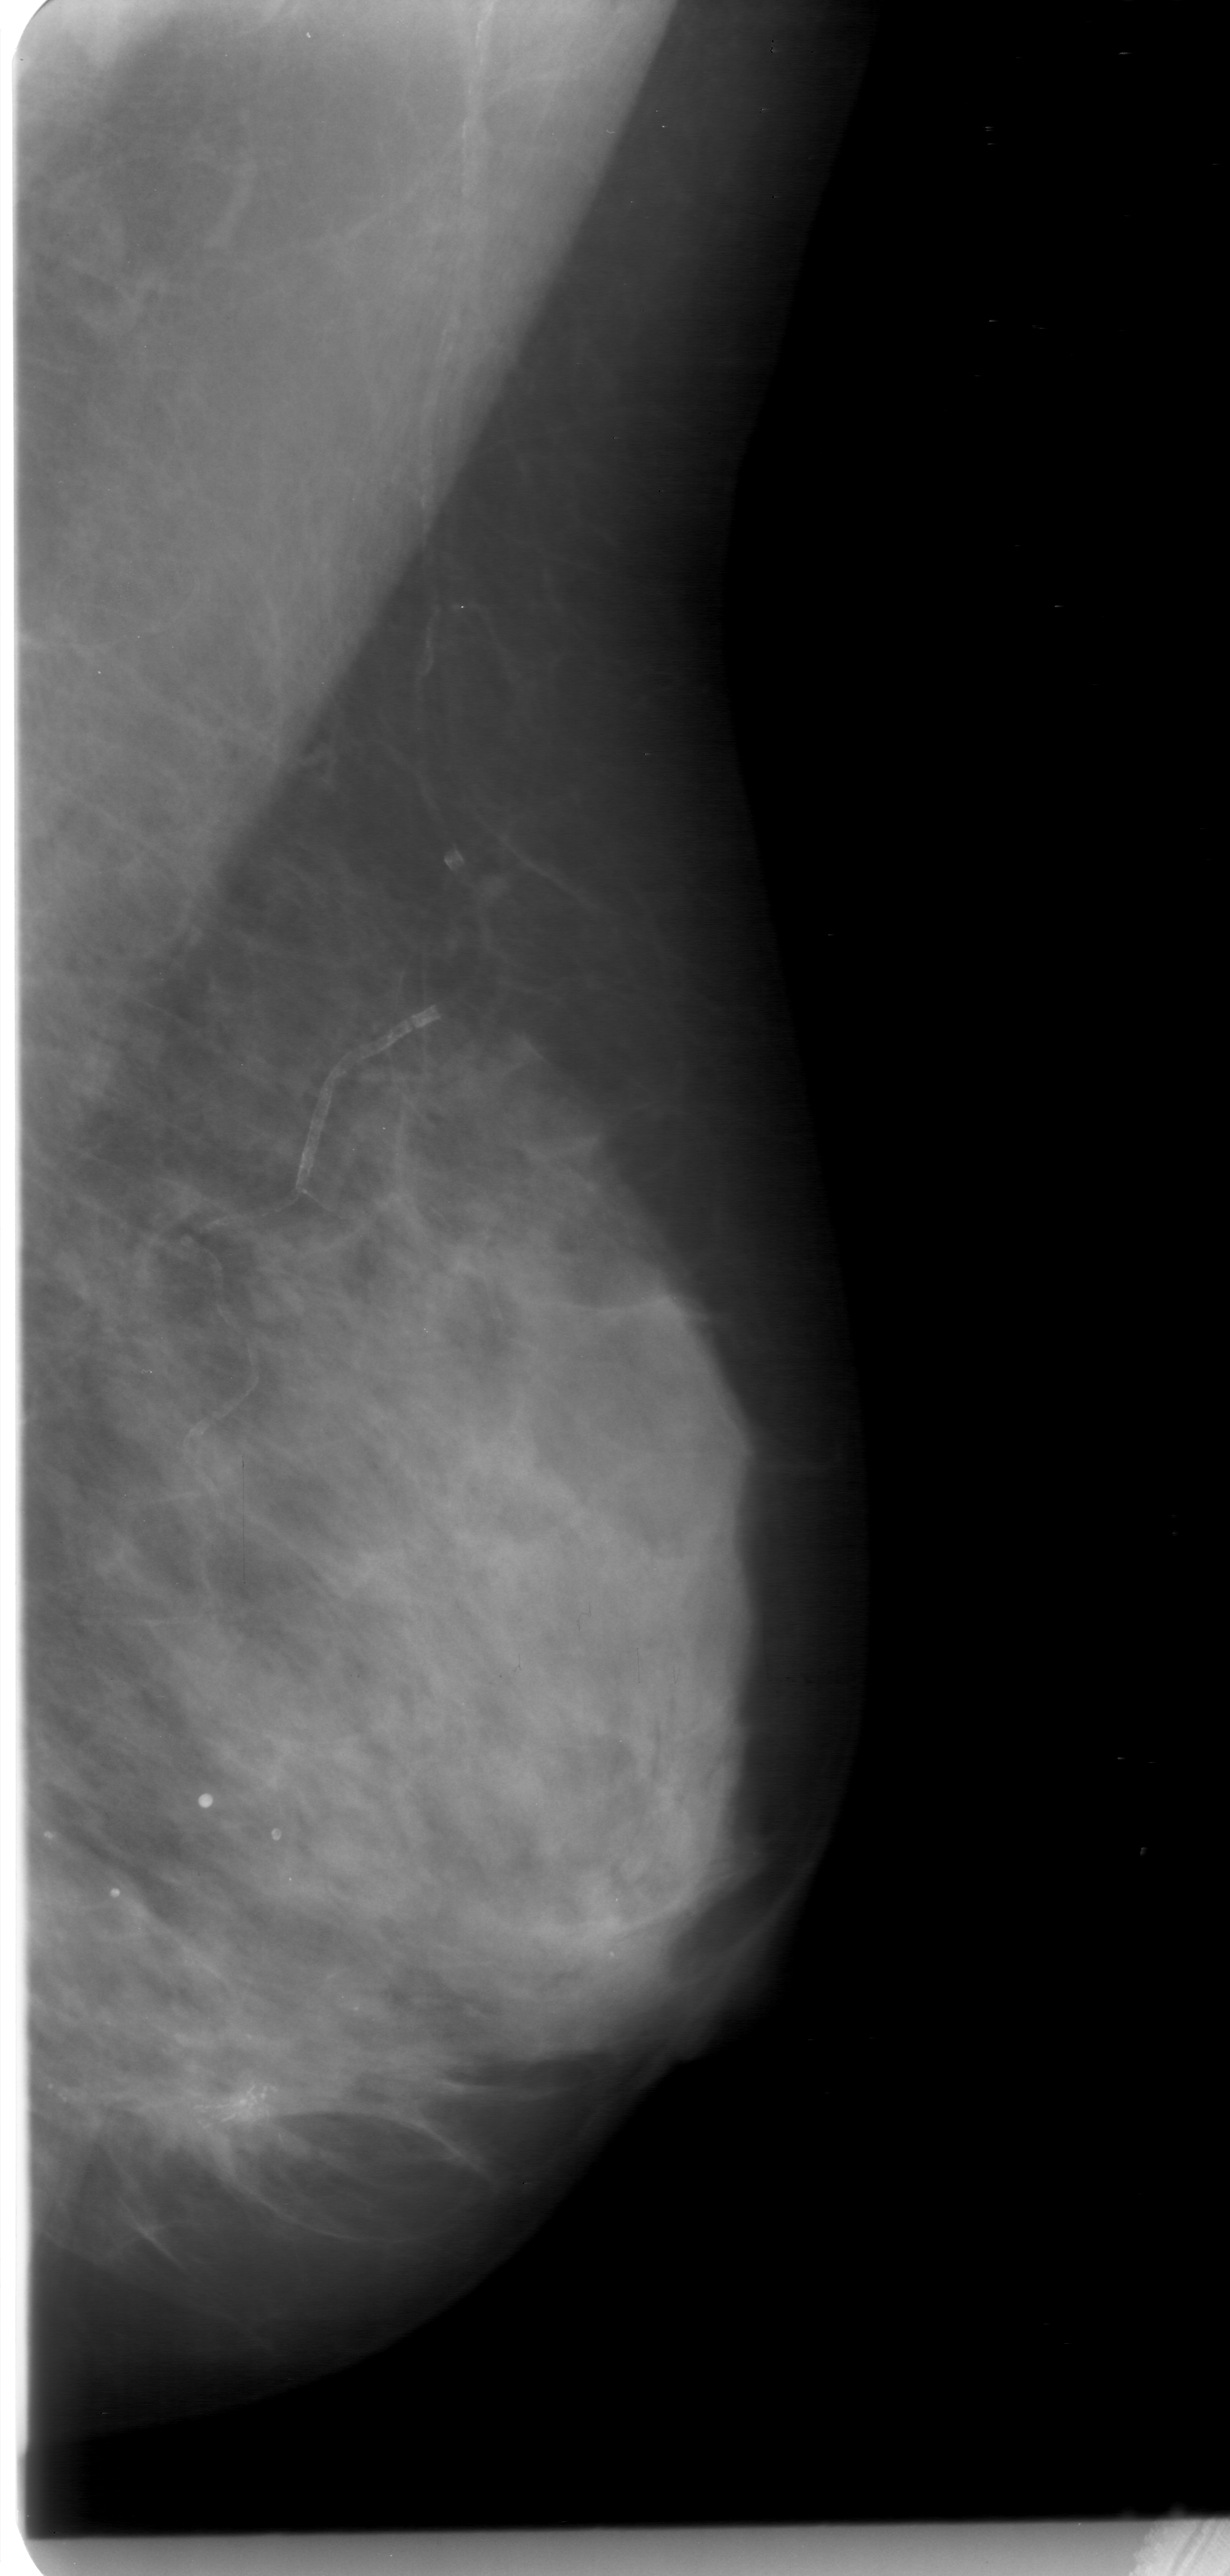
Mammogram (digitized film); left breast; MLO view; breast composition: heterogeneously dense (BI-RADS density category 3 of 4); 1230 × 2576 image matrix.
Expert-marked regions of interest on this image (one box per marked abnormality):
- calcifications, morphology fine linear branching, distribution clustered; BI-RADS assessment category 5; subtlety rating 4 on a 1 (subtle) to 5 (obvious) scale; pathology result (as recorded, not read from the image): malignant: box from (x=94, y=1953) to (x=462, y=2321) px